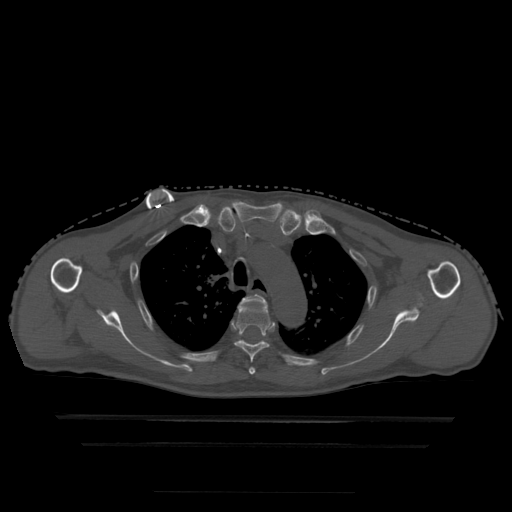
CT including the spine, one axial slice; position 355 of 522 along the scan axis; bone window (W 1800 / L 400 HU); 1.25 mm slice thickness; 512 × 512 image matrix, field of view 436 × 436 mm. Patient age 68 years. From the clinical record (not read from this slice): primary cancer: urothelial.
Annotated regions visible in this slice (semi-automatically segmented with operator editing):
- T3 vertebra: bounding box [x1, y1, x2, y2] px = [239, 294, 267, 375]
- T4 vertebra: [235, 303, 273, 375]